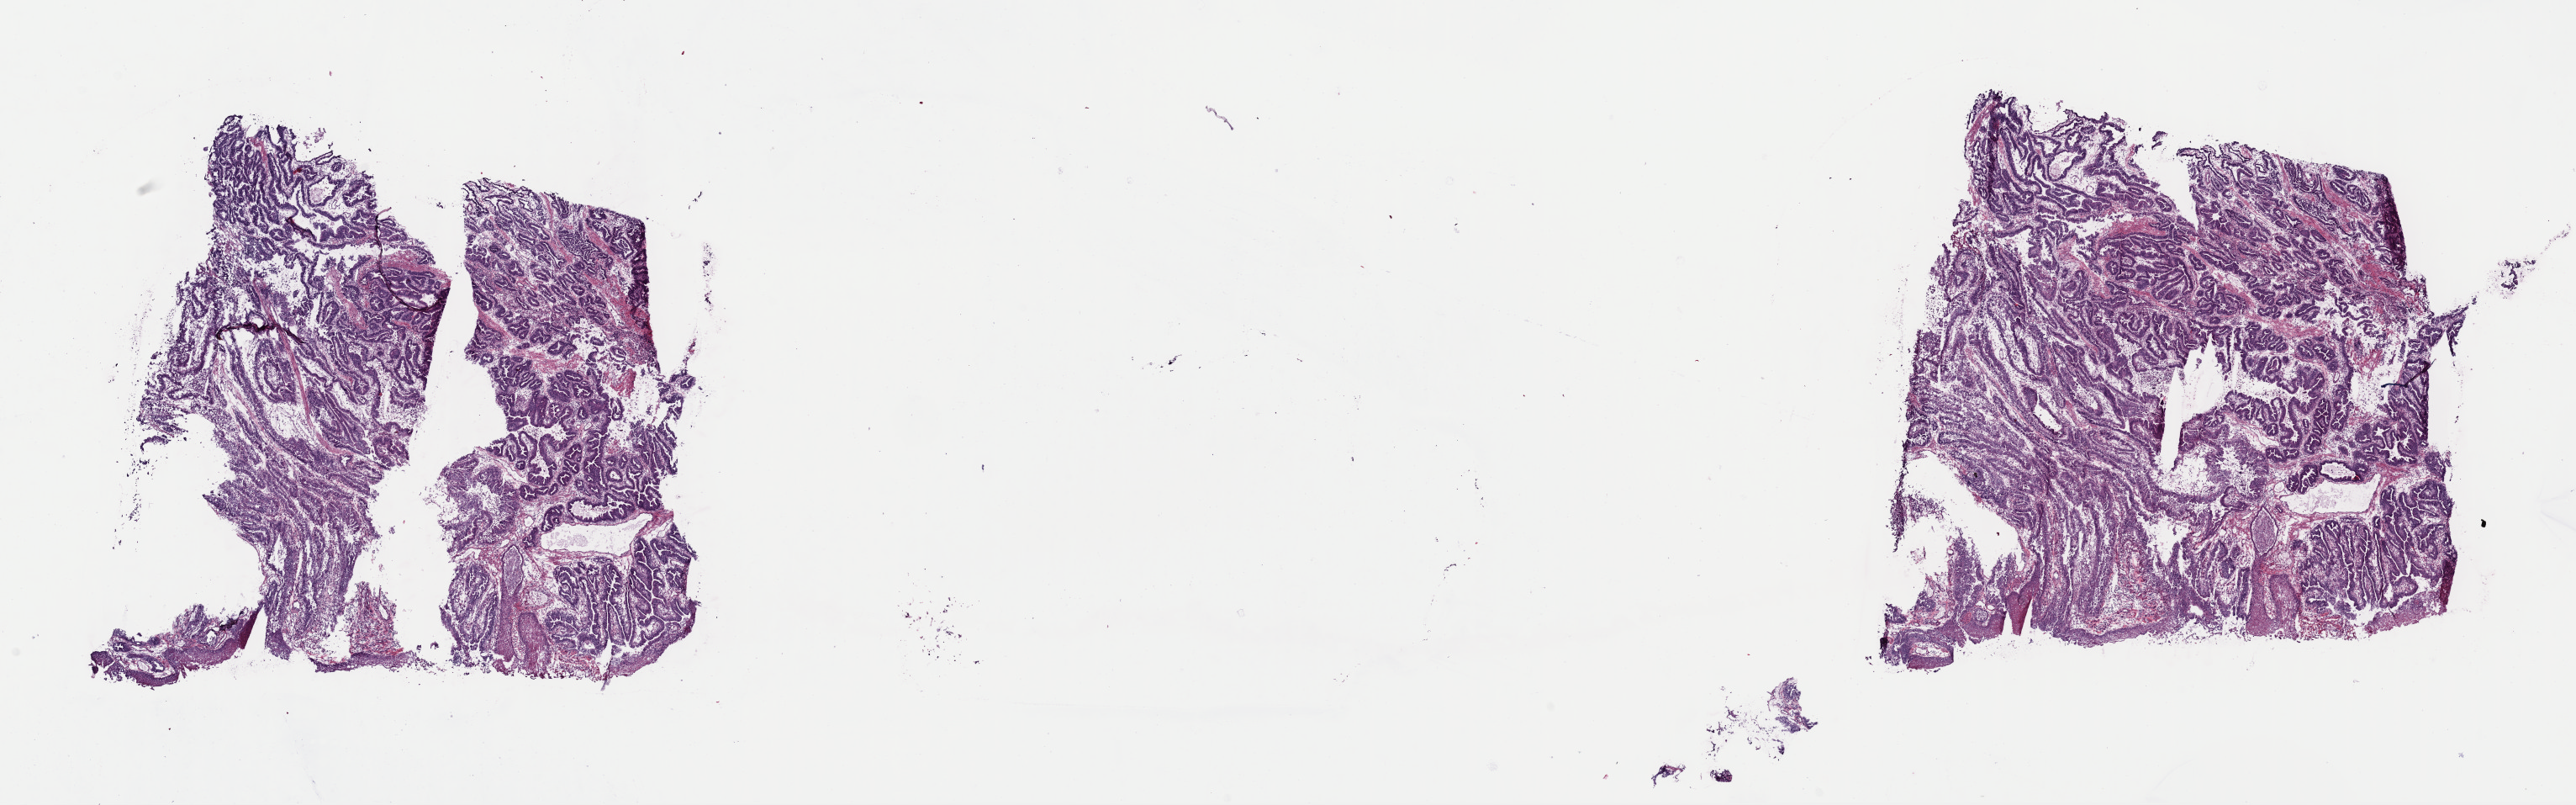
Whole-slide histology image, H&E-stained — whole scanned area (about 24.2 x 7.6 mm) shown as a low-resolution overview, frozen section from the top of the tissue portion, sample: primary tumour, esophagus. Male patient; age at initial diagnosis 65 years. Histologic grade: GX (grade cannot be assessed). Slide review estimates, as recorded: tumour cells 95%, tumour nuclei 80%, normal cells 5%, stromal cells 0%, necrosis 0%. Infiltration values recorded for this section: lymphocyte infiltration 4%, monocyte infiltration 0%, neutrophil infiltration 1%.
- AJCC pathologic stage: IIB
- lymph nodes positive (case pathology): 1 of 10 examined
- pathologic diagnosis: Adenocarcinoma, NOS (lower third of esophagus)